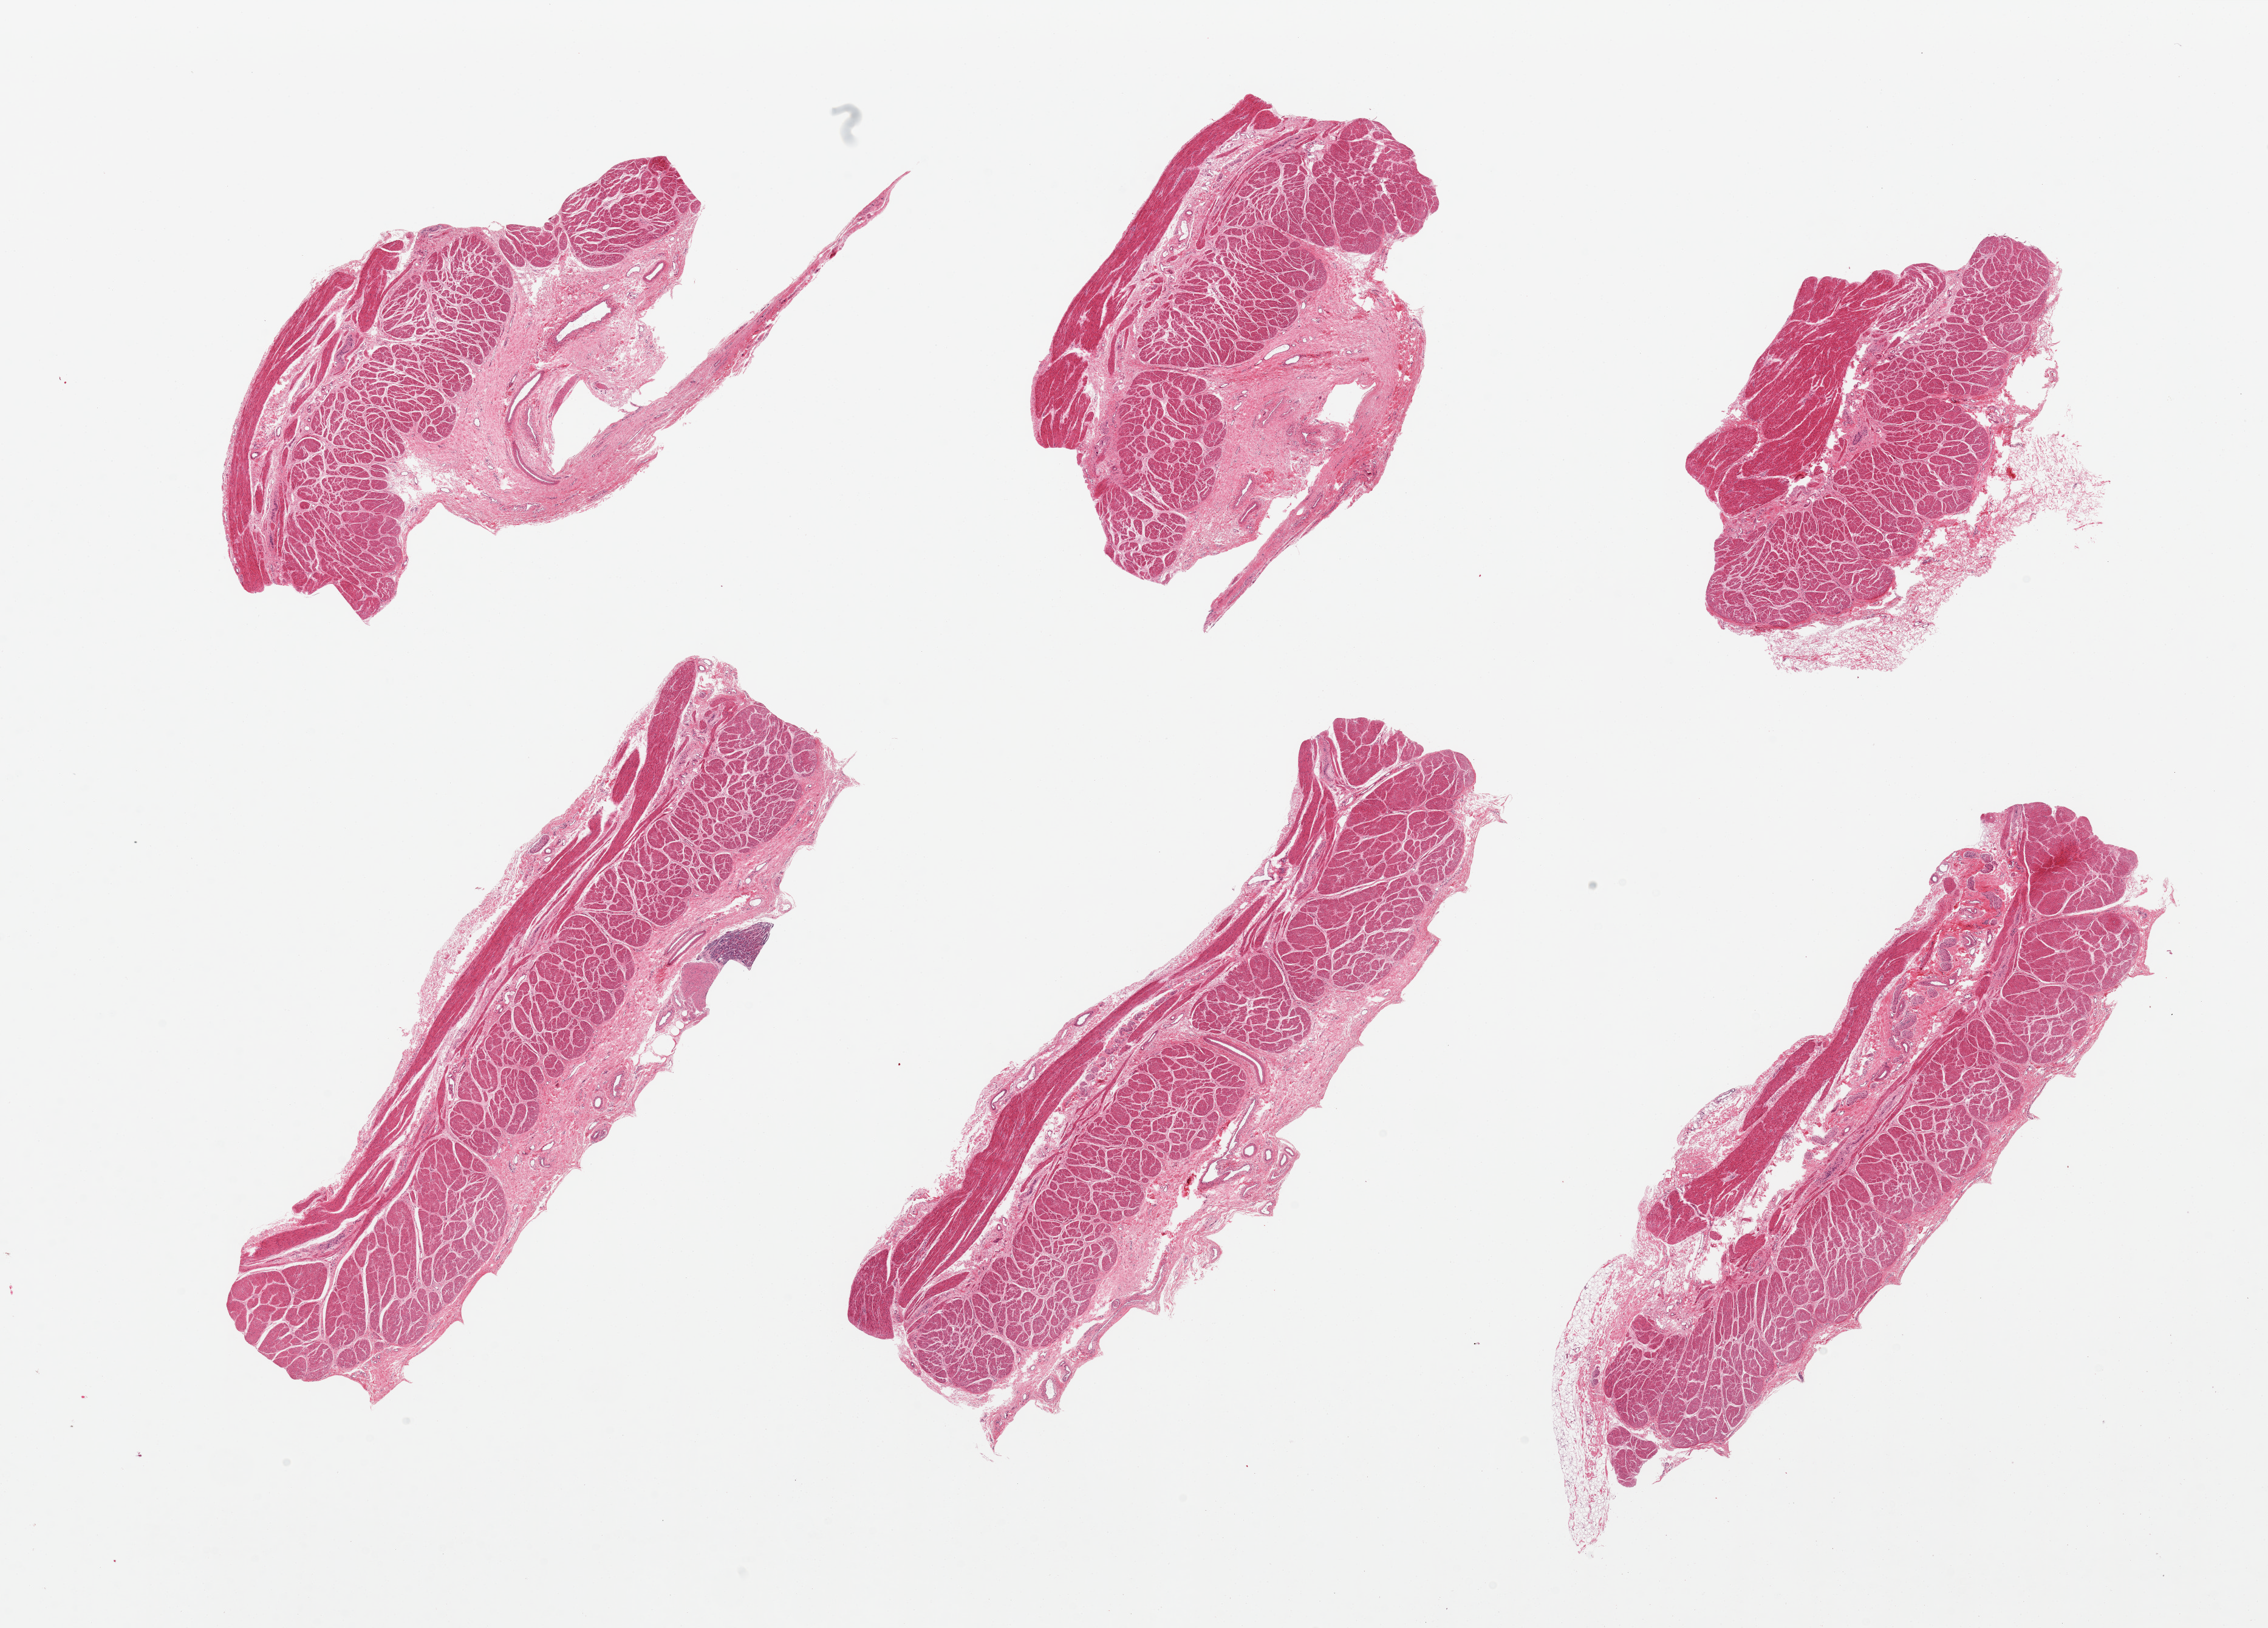
Digitized H&E-stained section — low-resolution overview of the scanned area, about 29.5 x 21.2 mm, PAXgene-fixed paraffin-embedded (PFPE) section, target tissue: gastroesophageal junction, donor tissue sample. Donor: female.
Pathologist's review note for this sample: 6 pieces, all muscularis/connective tissue, good specimens; Minute (0.5mm) fragement of 'contaminant' gastric mucoa adjacent to one section.